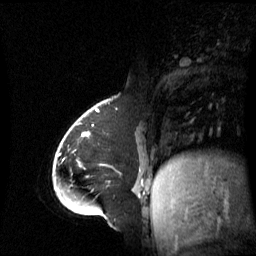
Breast MRI (dynamic contrast-enhanced), one sagittal slice; slice 20 of 60 in the series (ordered by position); dynamic contrast-enhanced series, image 2 of 3 at this slice position (ordered by acquisition); 1.5 T; TE 4.2 ms, TR 8.4 ms; 2.8 mm slice thickness; 256 × 256 image matrix. Female patient, age 43 years. Case-level facts recorded for this patient, not image findings: setting: breast cancer imaged before/during neoadjuvant chemotherapy; receptor status: triple-negative.
Outlined on this slice (semi-automatic segmentation, software-assisted and operator-edited):
- analysis volume of interest (the breast-tissue region the enhancement analysis was run in; not a lesion): bounding box [x1, y1, x2, y2] px = [65, 118, 143, 198]
- tumour enhancement mask (voxels above the 70 % enhancement threshold inside the analysis volume of interest): [87, 133, 140, 197]